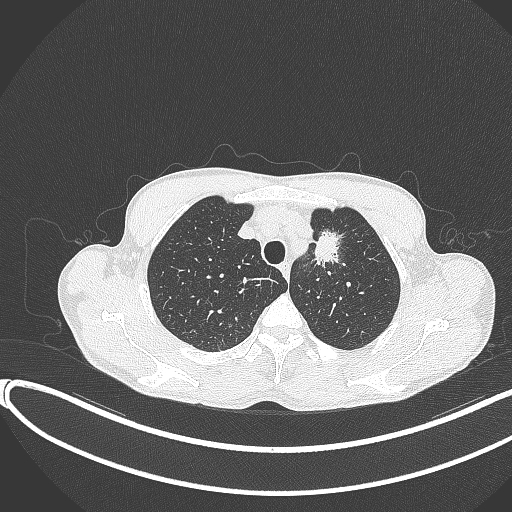
Chest CT, one axial slice; slice 314 of 374 in the series (ordered by position); 120 kVp; lung window (W 1500 / L -600 HU); 1 mm slice thickness; 512 × 512 image matrix, field of view 400 × 400 mm. Male patient, age 58 years. Case-level facts recorded for this patient, not image findings: clinical TNM (as recorded): T1c N1 M0.
Annotated regions visible in this slice (bounding box drawn by a radiologist):
- lung tumour (recorded histology: adenocarcinoma): box from (x=310, y=228) to (x=356, y=280) px